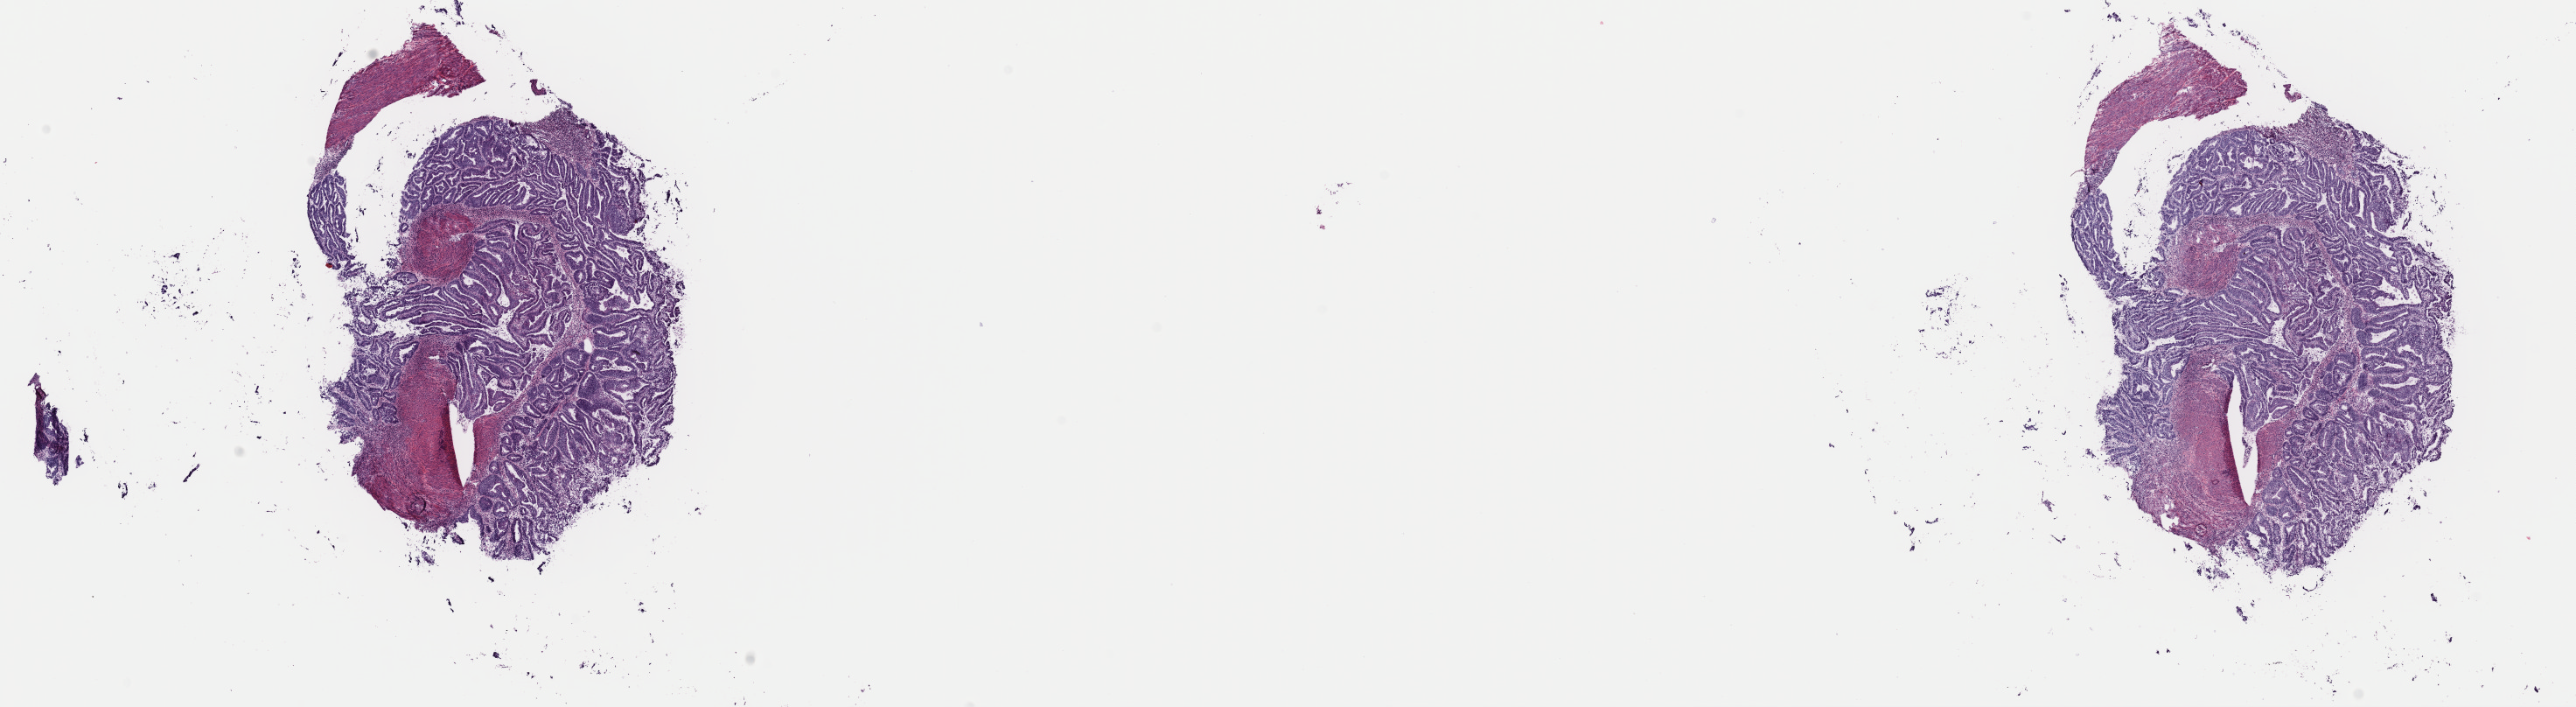
Whole-slide histology image, H&E-stained — low-resolution overview of the scanned area, about 23.3 x 6.4 mm. Frozen section from the top of the tissue portion. Primary tumour sample from the uterus. Female, age 62 years at initial diagnosis. Histologic grade: G2 (moderately differentiated). Pathologist review of this section (percent, as recorded): tumour cells 75%, tumour nuclei 75%, normal cells 15%, stromal cells 10%, necrosis 0%. Infiltration values recorded for this section: lymphocyte infiltration 5%, monocyte infiltration 2%, neutrophil infiltration 2%.
FIGO stage: IA. Histologic diagnosis: Endometrioid adenocarcinoma, NOS (endometrium).